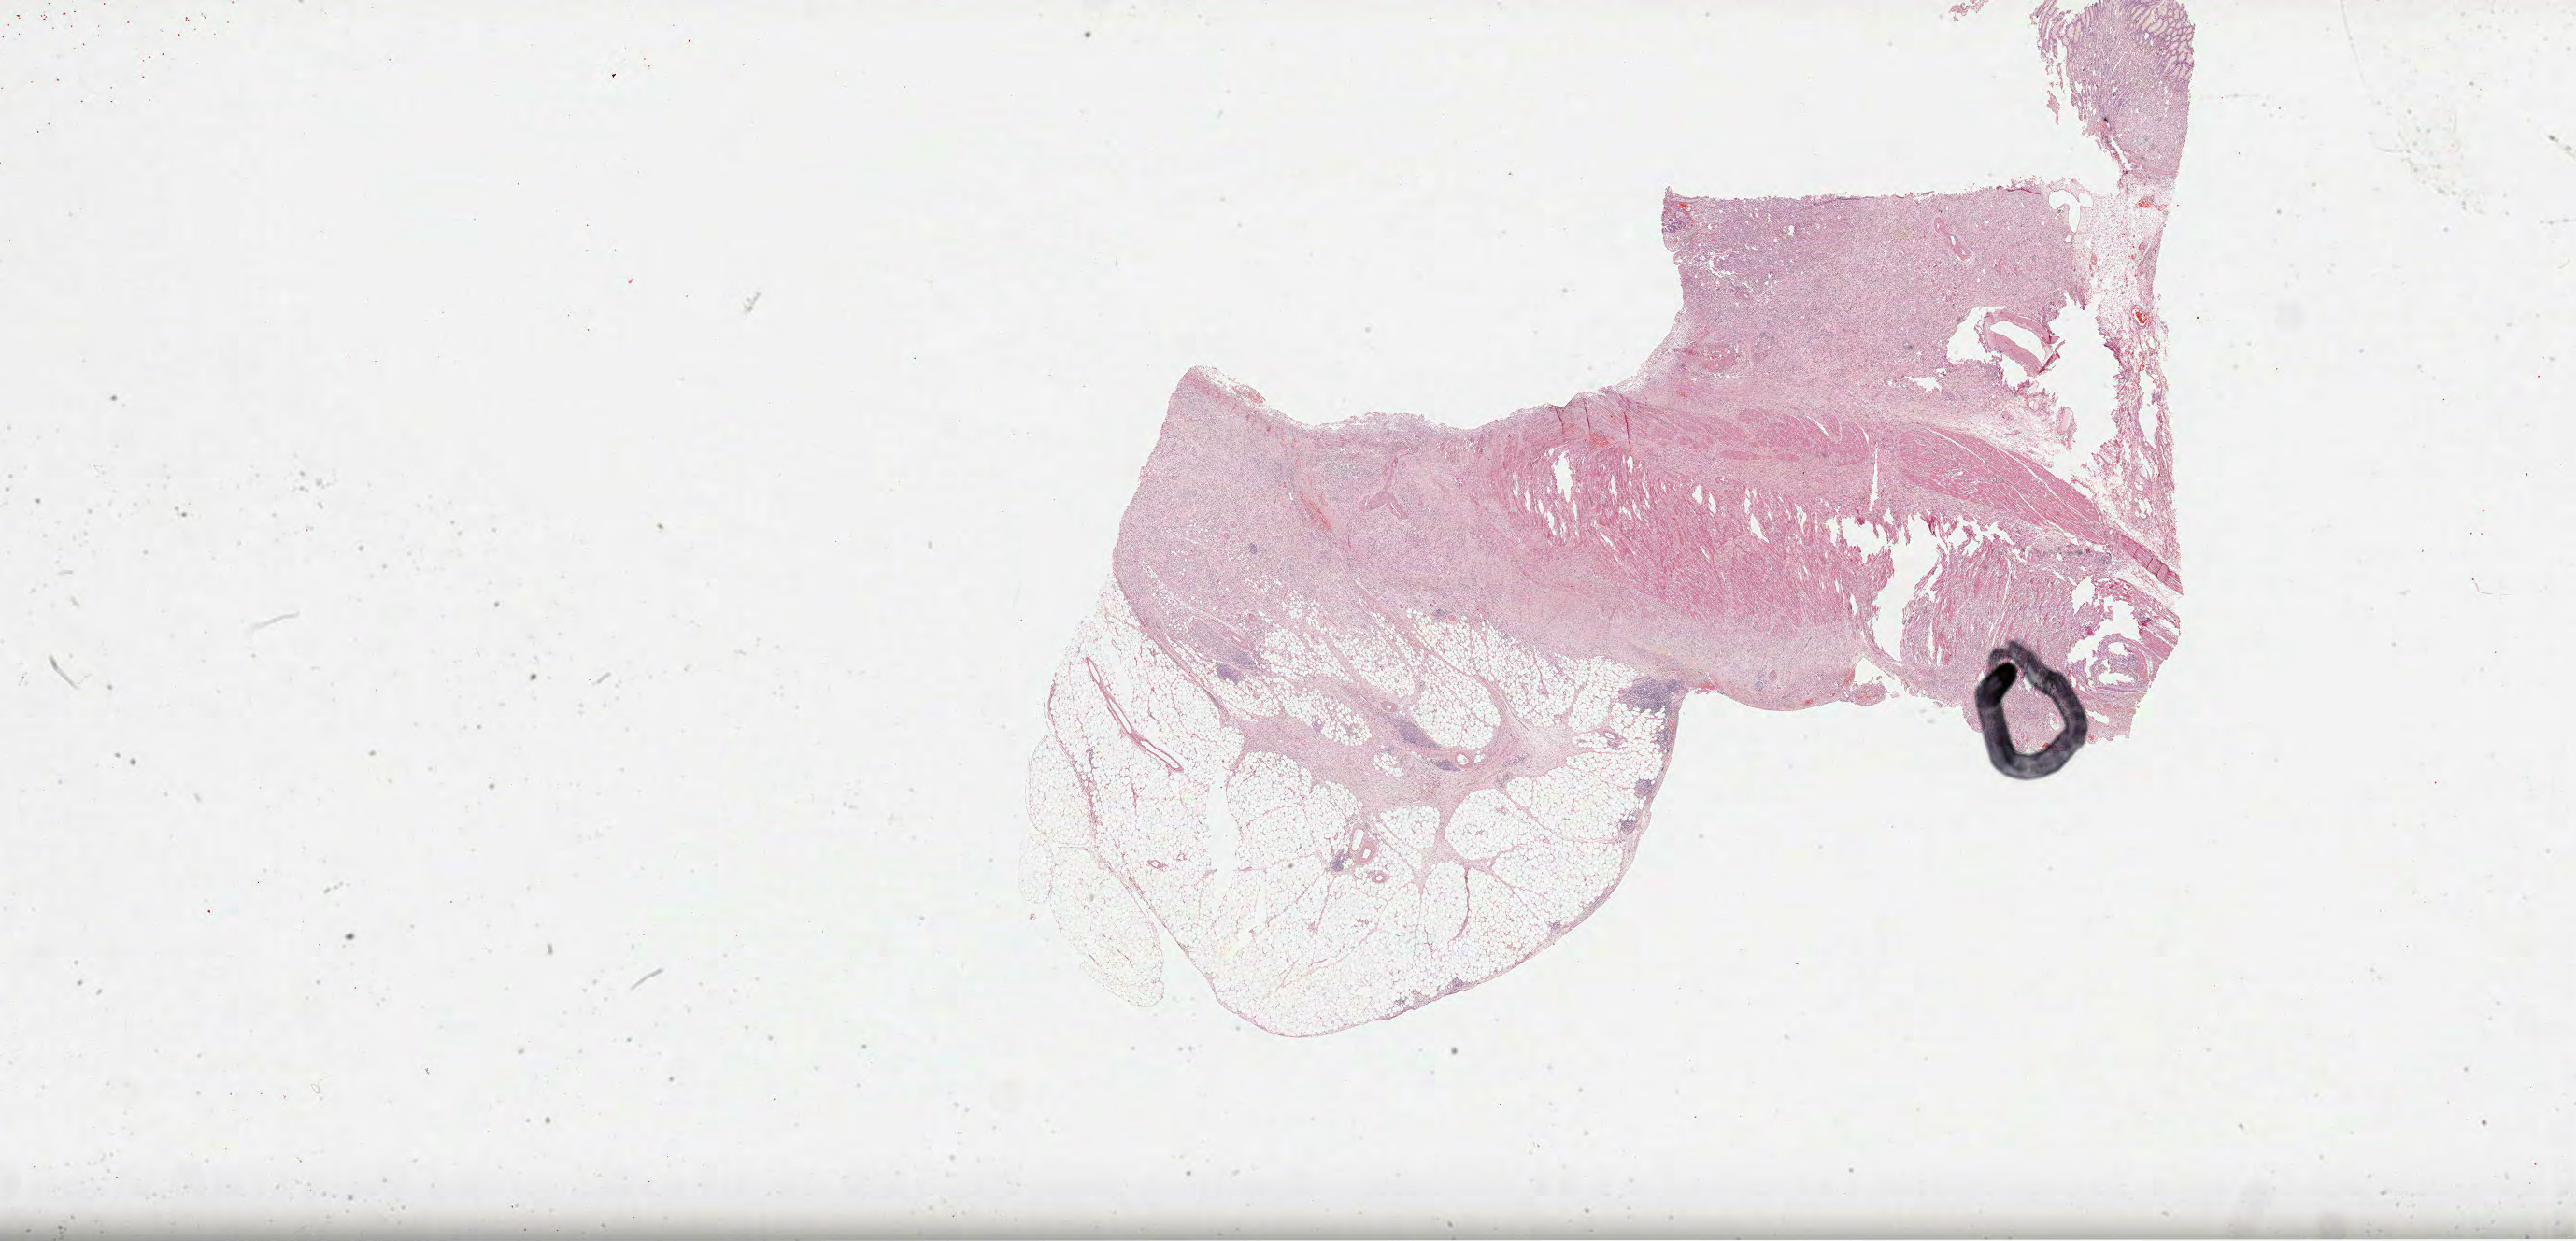
H&E whole-slide image, whole scanned area (about 44.5 x 21.4 mm) shown as a low-resolution overview. Formalin-fixed paraffin-embedded (FFPE) diagnostic section. Stomach, primary tumour sample. Male, age 65 years at initial diagnosis. Histologic grade: G3 (poorly differentiated).
Pathologic diagnosis: Carcinoma, diffuse type.